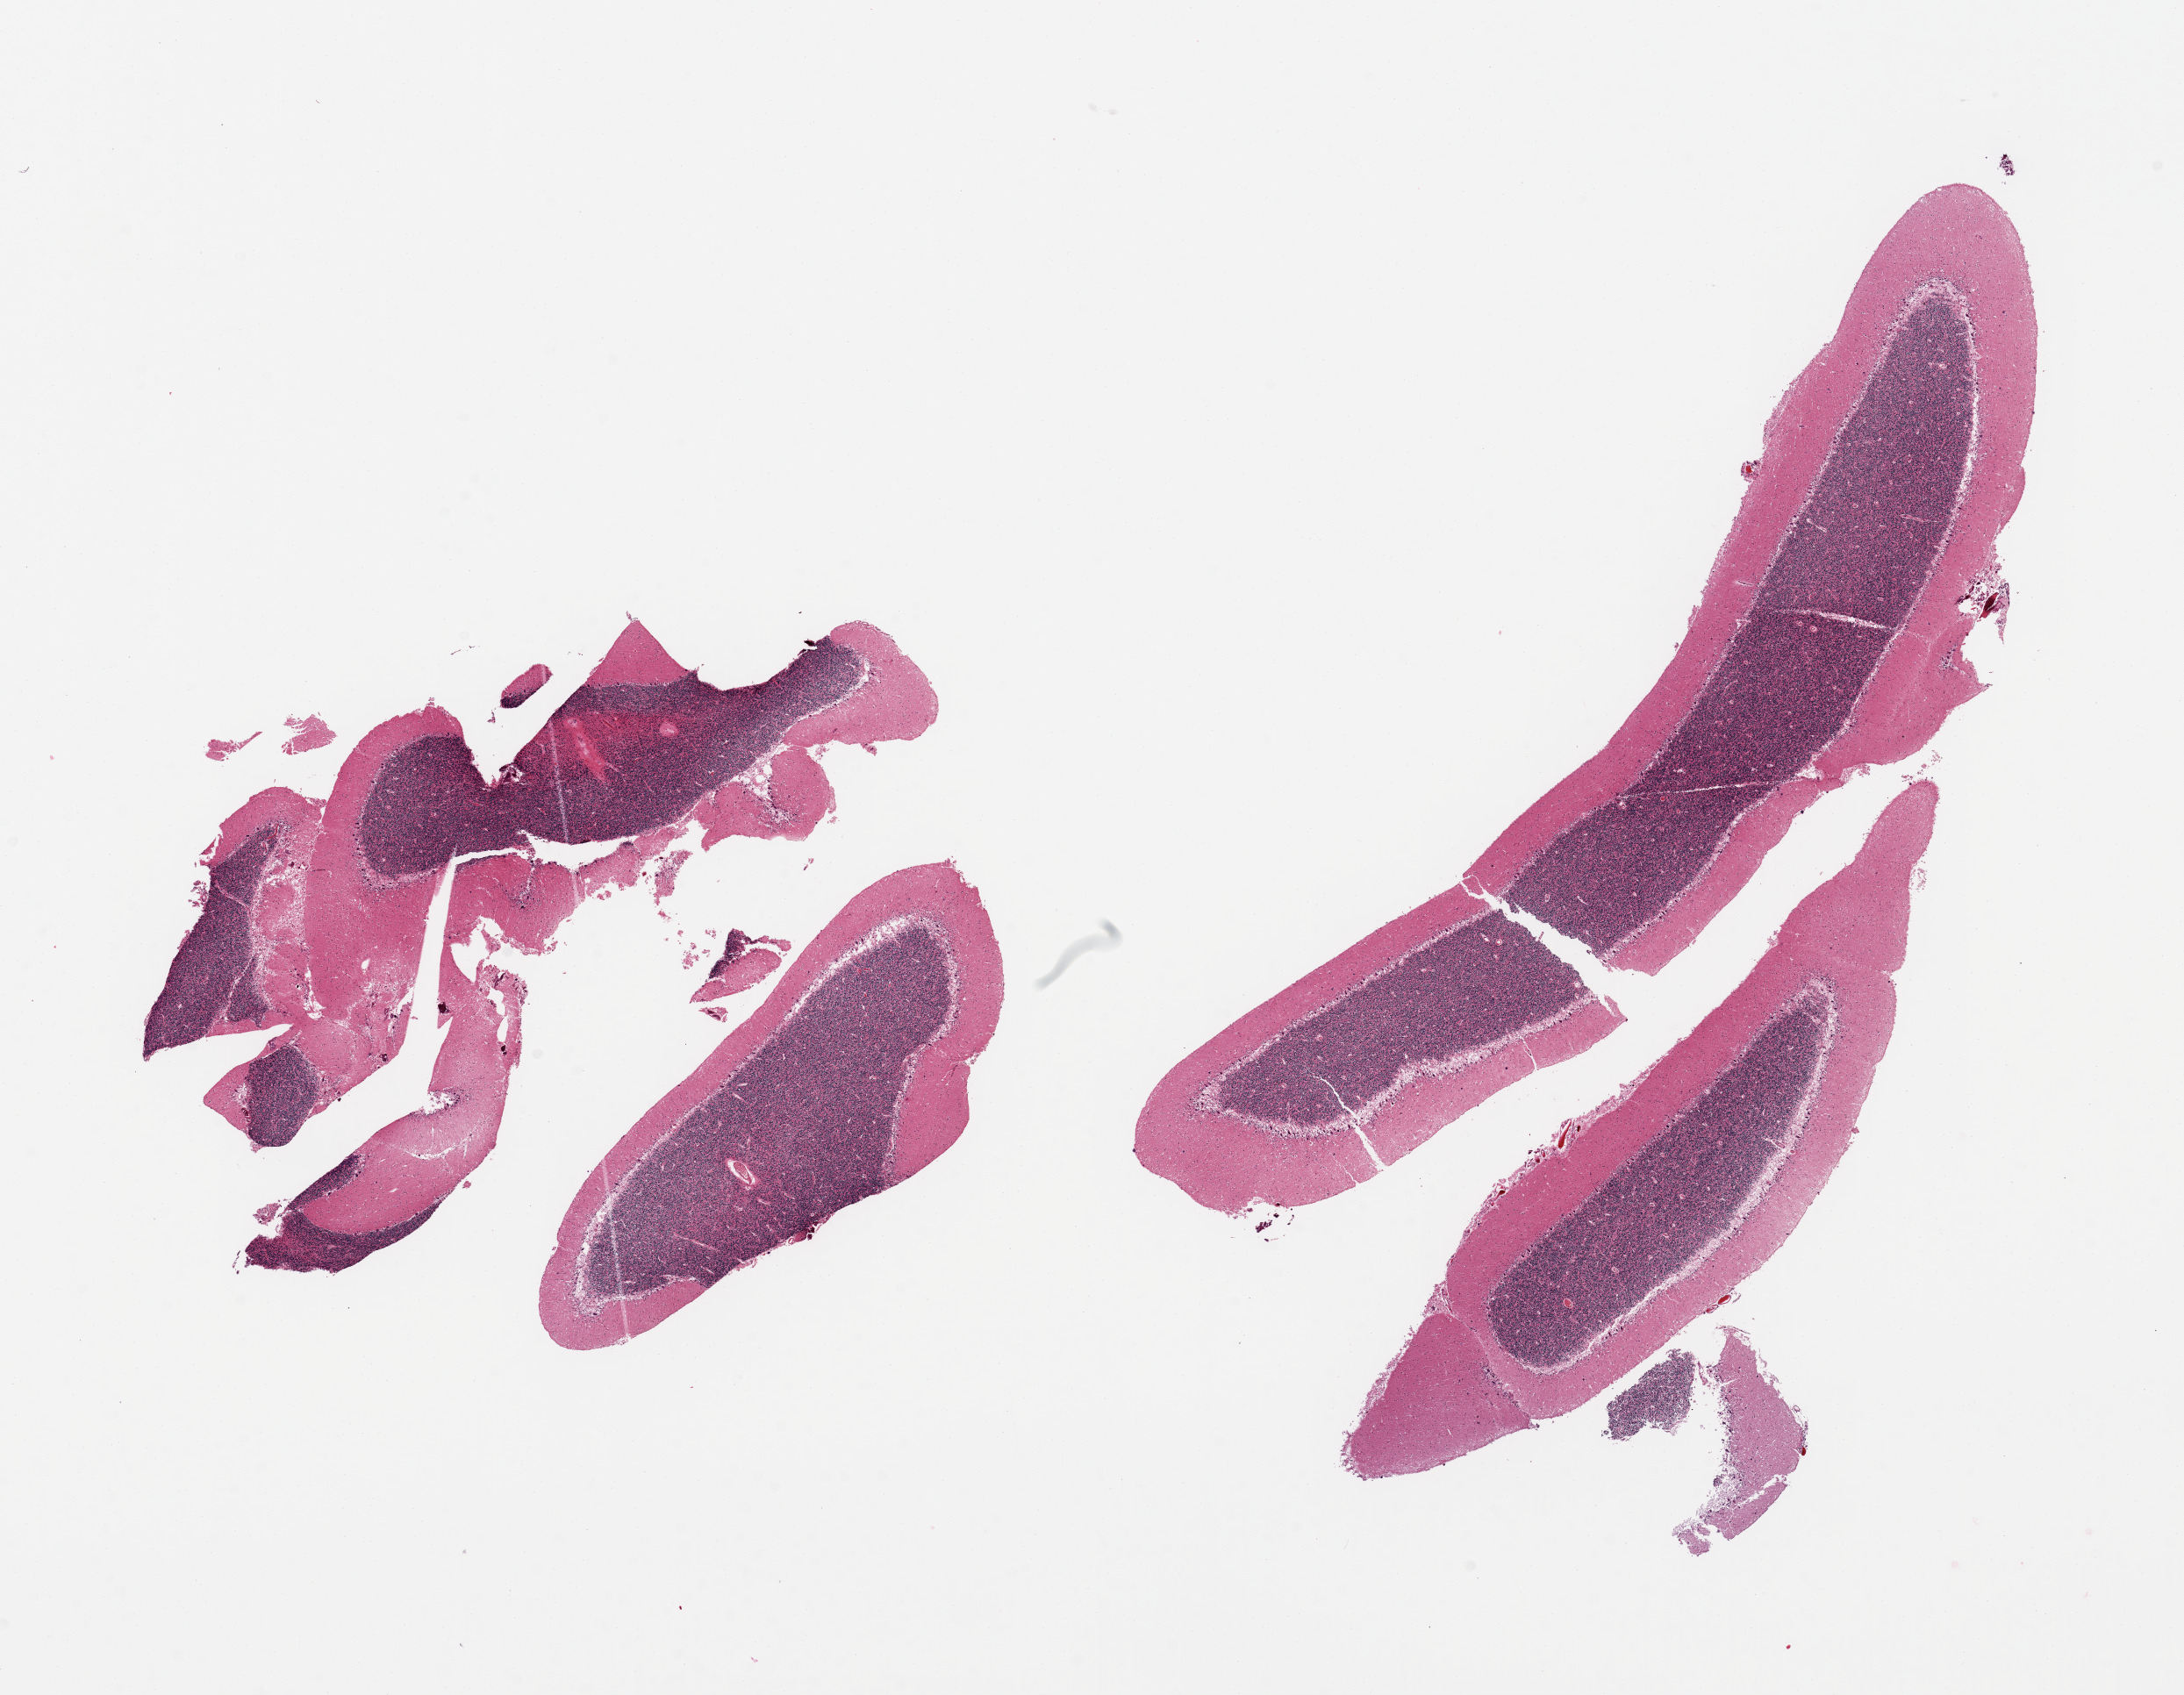
H&E whole-slide image — shown as a low-resolution overview of the whole scanned area (about 19.7 x 15.3 mm); PAXgene-fixed, paraffin-embedded tissue; target tissue: cerebellum; donor tissue sample. Male donor.
Reviewer comment on this tissue sample: 2 pieces (fragmented), no abnormalities.